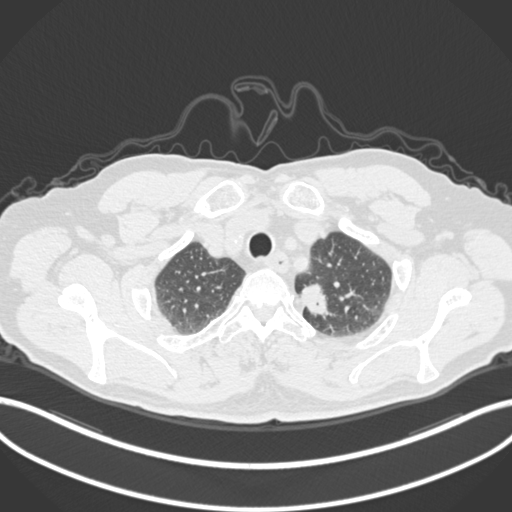
Chest CT, one axial slice; slice 280 of 306 in the series (ordered by position); reconstruction kernel B30f; 120 kVp; lung window (W 1500 / L -600 HU); 1 mm slice thickness; 512 × 512 image matrix. Patient: male, 64 years. From the clinical record (not read from this slice): clinical TNM (as recorded): T1c N0 M0.
Outlined on this slice (rectangle marked by the reading radiologist):
- lung tumour (recorded histology: adenocarcinoma): box from (x=296, y=281) to (x=333, y=322) px